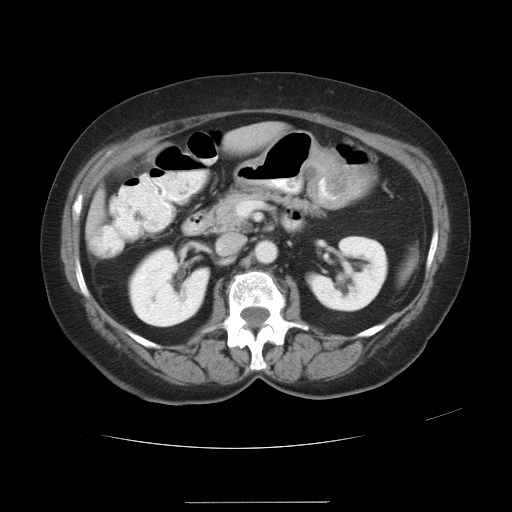
Contrast-enhanced abdominal CT, one axial slice; slice 13 of 32 in the series (ordered by position); reconstruction kernel STANDARD; intravenous contrast given; soft-tissue window (W 400 / L 40 HU); 512 × 512 image matrix, field of view 386 × 386 mm. Female patient, age 65 years. Case-level facts recorded for this patient, not image findings: diagnosis: colorectal cancer liver metastases, imaged before liver resection; multiple liver metastases: yes; largest metastasis: 1.7 cm; disease in both lobes: no.
Annotated regions visible in this slice (expert manual segmentation):
- liver: bounding box (x1, y1, x2, y2) in pixels: (230, 128, 270, 146)